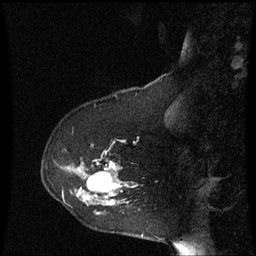
Breast MRI (dynamic contrast-enhanced), one sagittal slice; position 18 of 60 along the scan axis; dynamic contrast-enhanced series, image 2 of 3 at this slice position (ordered by acquisition); 1.5 T; TE 4.2 ms, TR 8.9 ms; 2 mm slice thickness; 256 × 256 image matrix, field of view 200 × 200 mm. Female patient, age 53 years. From the clinical record (not read from this slice): setting: breast cancer imaged before/during neoadjuvant chemotherapy; receptor status: HR-positive, HER2-negative.
Outlined on this slice (semi-automatically segmented with operator editing):
- analysis volume of interest (the breast-tissue region the enhancement analysis was run in; not a lesion): bounding box [x1, y1, x2, y2] px = [42, 144, 149, 221]
- tumour enhancement mask (voxels above the 70 % enhancement threshold inside the analysis volume of interest): [78, 162, 119, 205]